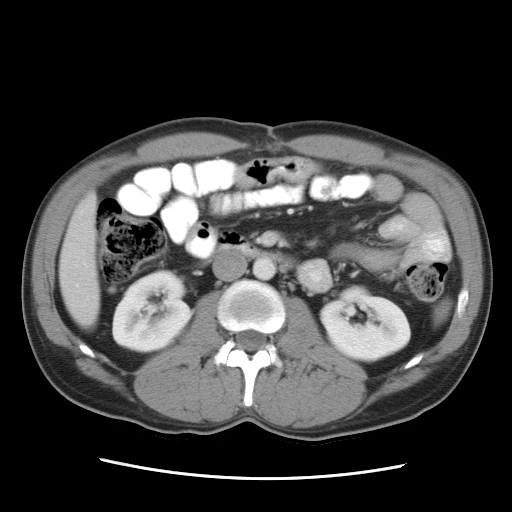
Contrast-enhanced abdominal CT, one axial slice; slice 9 of 34 in the series (ordered by position); reconstruction kernel STANDARD; 120 kVp; intravenous contrast given; soft-tissue window (W 400 / L 40 HU); 7.5 mm slice thickness; 512 × 512 image matrix, field of view 360 × 360 mm. Male patient, age 40 years. Case-level facts recorded for this patient, not image findings: diagnosis: colorectal cancer liver metastases, imaged before liver resection; multiple liver metastases: yes; largest metastasis: 1.5 cm; disease in both lobes: yes.
Structures marked on this image (outlined manually by an expert reader):
- liver: bounding box [x1, y1, x2, y2] px = [61, 193, 100, 323]
- planned liver remnant (the part of the liver to remain after resection): [75, 193, 97, 227]